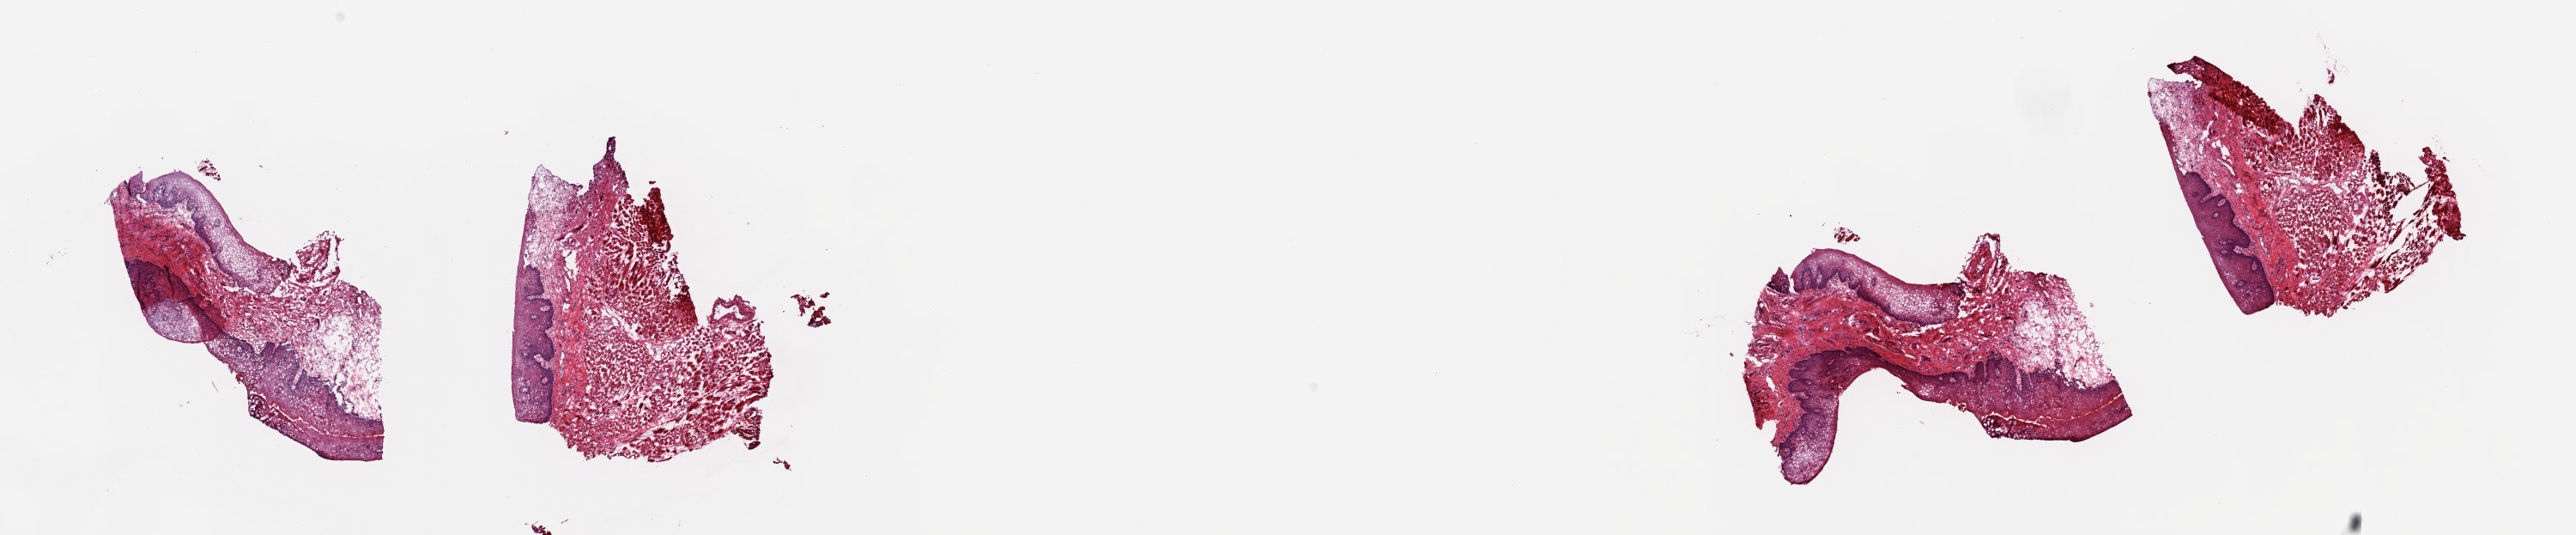
H&E whole-slide image — low-resolution overview of the scanned area, about 23.8 x 4.9 mm. Frozen section. Head and neck, solid tissue normal (non-tumour tissue) sample. Male patient; age at initial diagnosis 58 years. Slide review estimates, as recorded: tumour cells 0%, tumour nuclei 0%, normal cells 100%, stromal cells 0%, necrosis 0%. Inflammatory infiltration, as recorded: lymphocyte infiltration 0%, monocyte infiltration 0%, neutrophil infiltration 0%.
This section: solid tissue normal (non-tumour) sample from the same patient. Patient diagnosis: Squamous cell carcinoma, keratinizing, NOS.